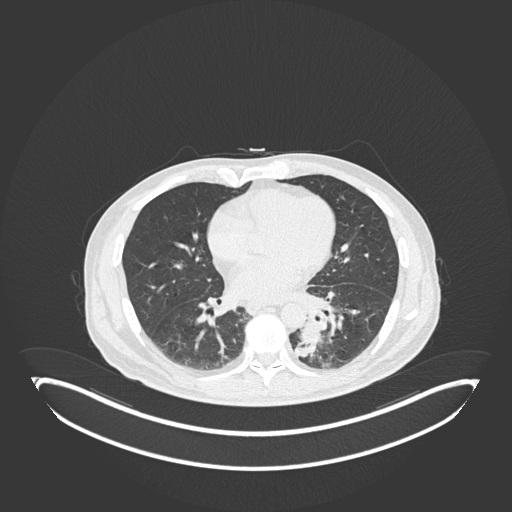
Chest CT, one axial slice. Position 72 of 251 along the scan axis. Reconstruction kernel B30f. 120 kVp. Lung window (W 1500 / L -600 HU). 1 mm slice thickness. 512 × 512 image matrix, field of view 500 × 500 mm. Male patient, age 72 years. From the clinical record (not read from this slice): clinical TNM (as recorded): T2b N0 M1.
Outlined on this slice (rectangle marked by the reading radiologist):
- lung tumour (recorded histology: adenocarcinoma): box from (x=287, y=316) to (x=323, y=359) px